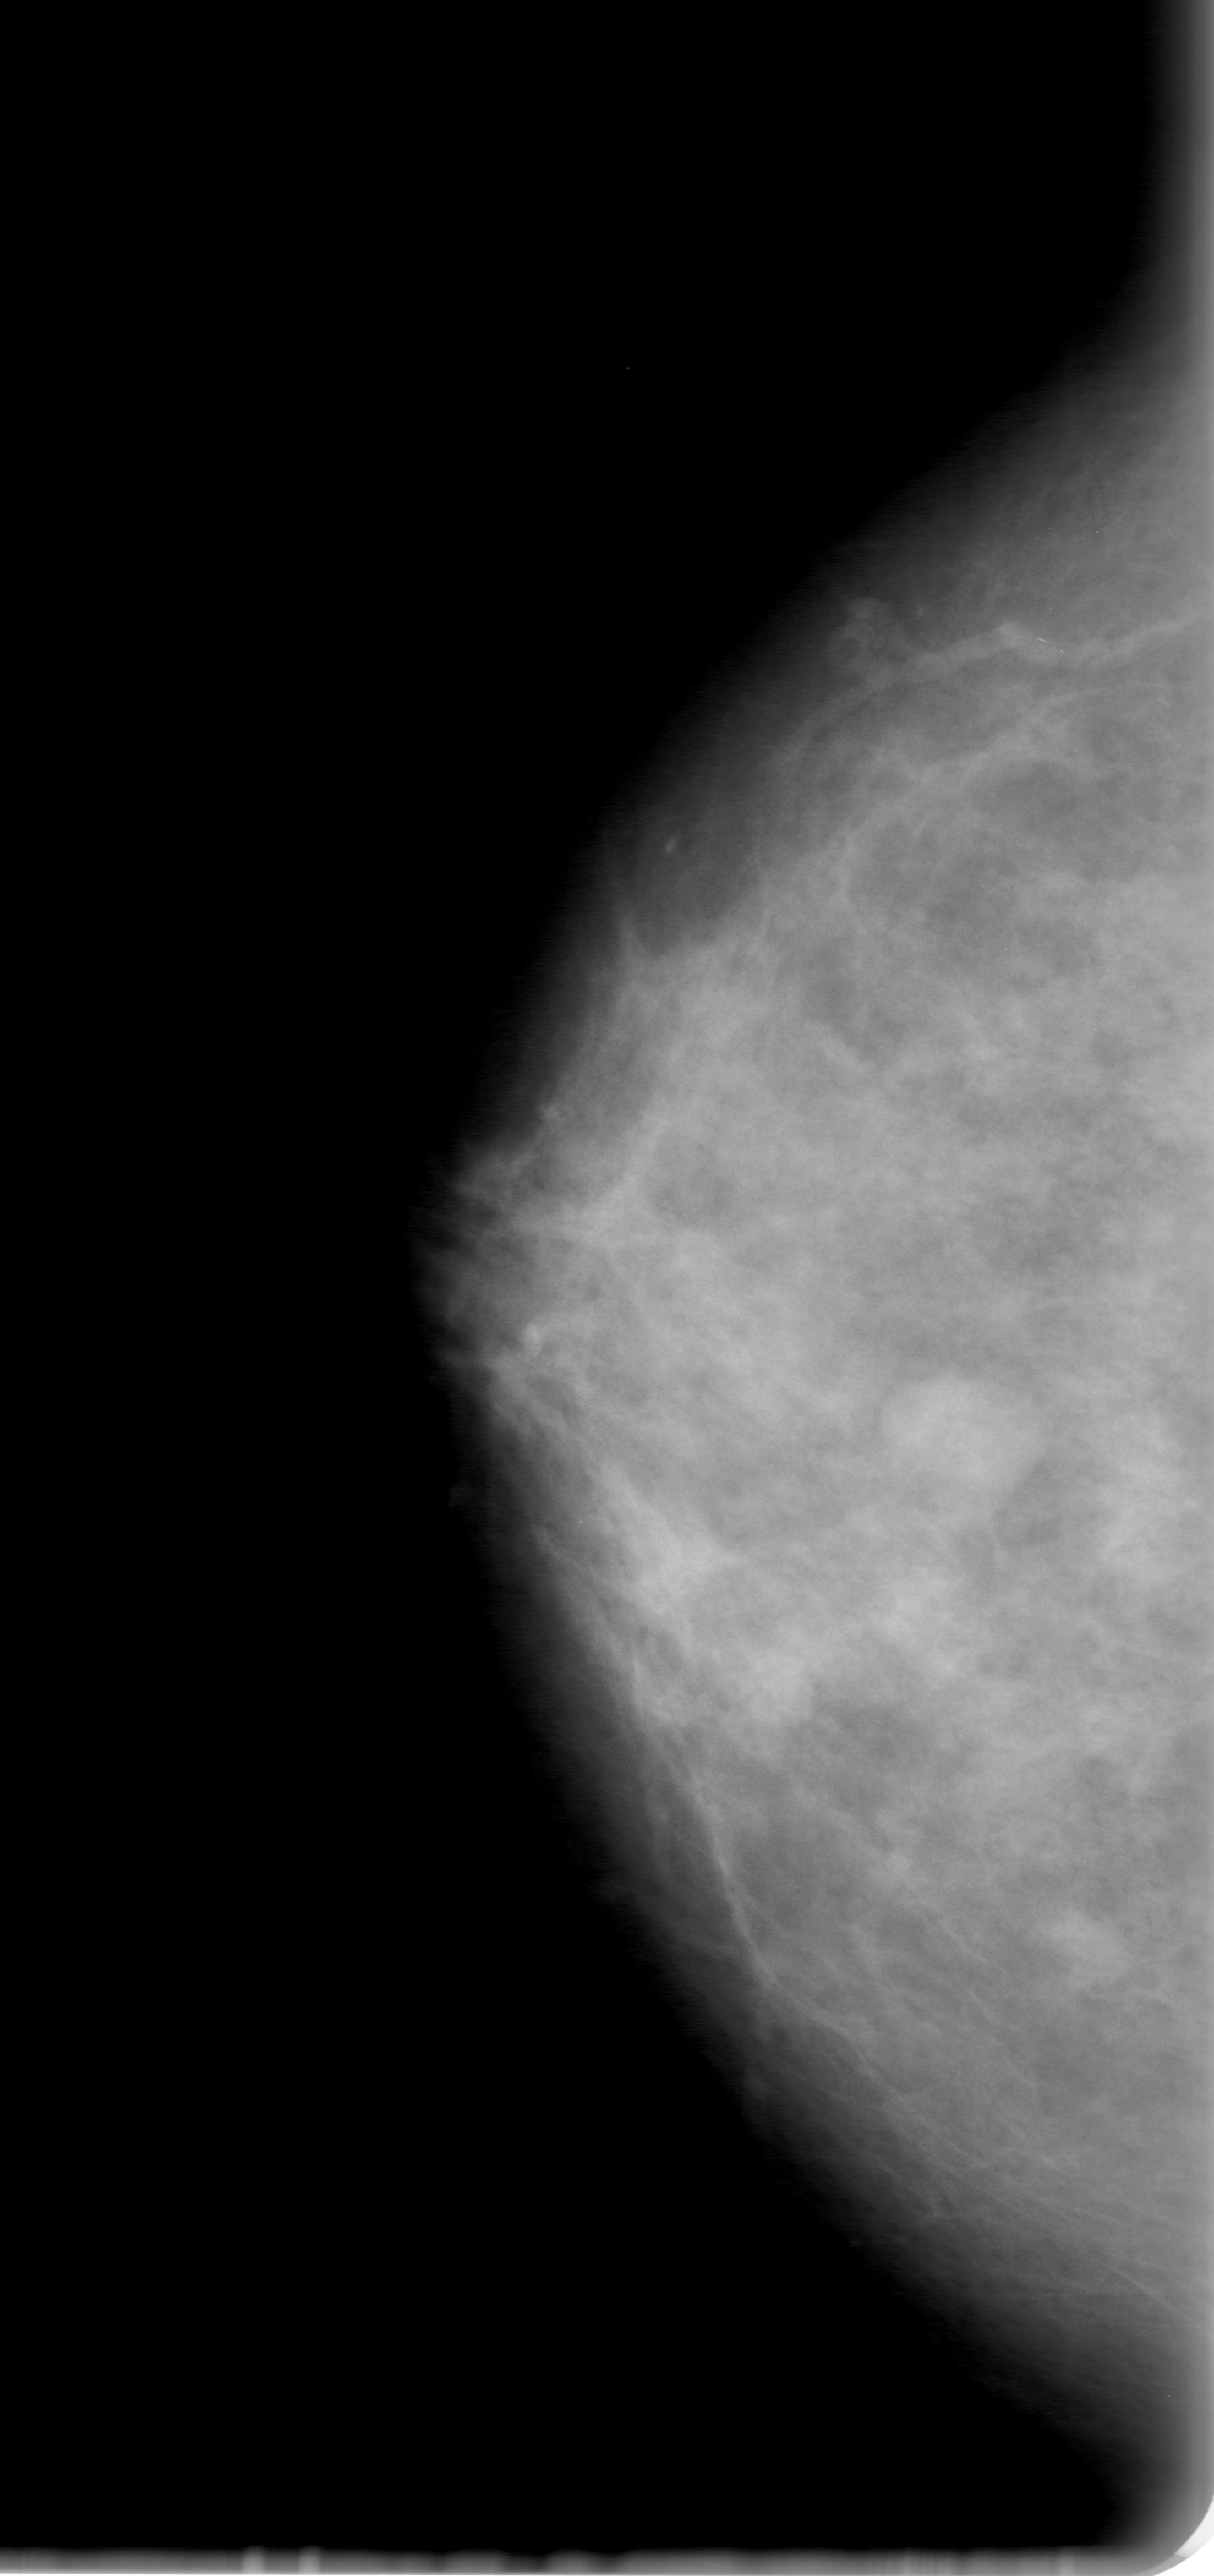
Scanned film-screen mammogram; right breast; CC view; breast composition: scattered fibroglandular densities (BI-RADS density category 2 of 4).
Marked findings (only marked abnormalities are described; nothing is implied about the rest of the image): mass, shape oval, margins microlobulated; BI-RADS assessment category 0 (incomplete: needs additional imaging); subtlety rating 4 on a 1 (subtle) to 5 (obvious) scale; pathology result (as recorded, not read from the image): benign.